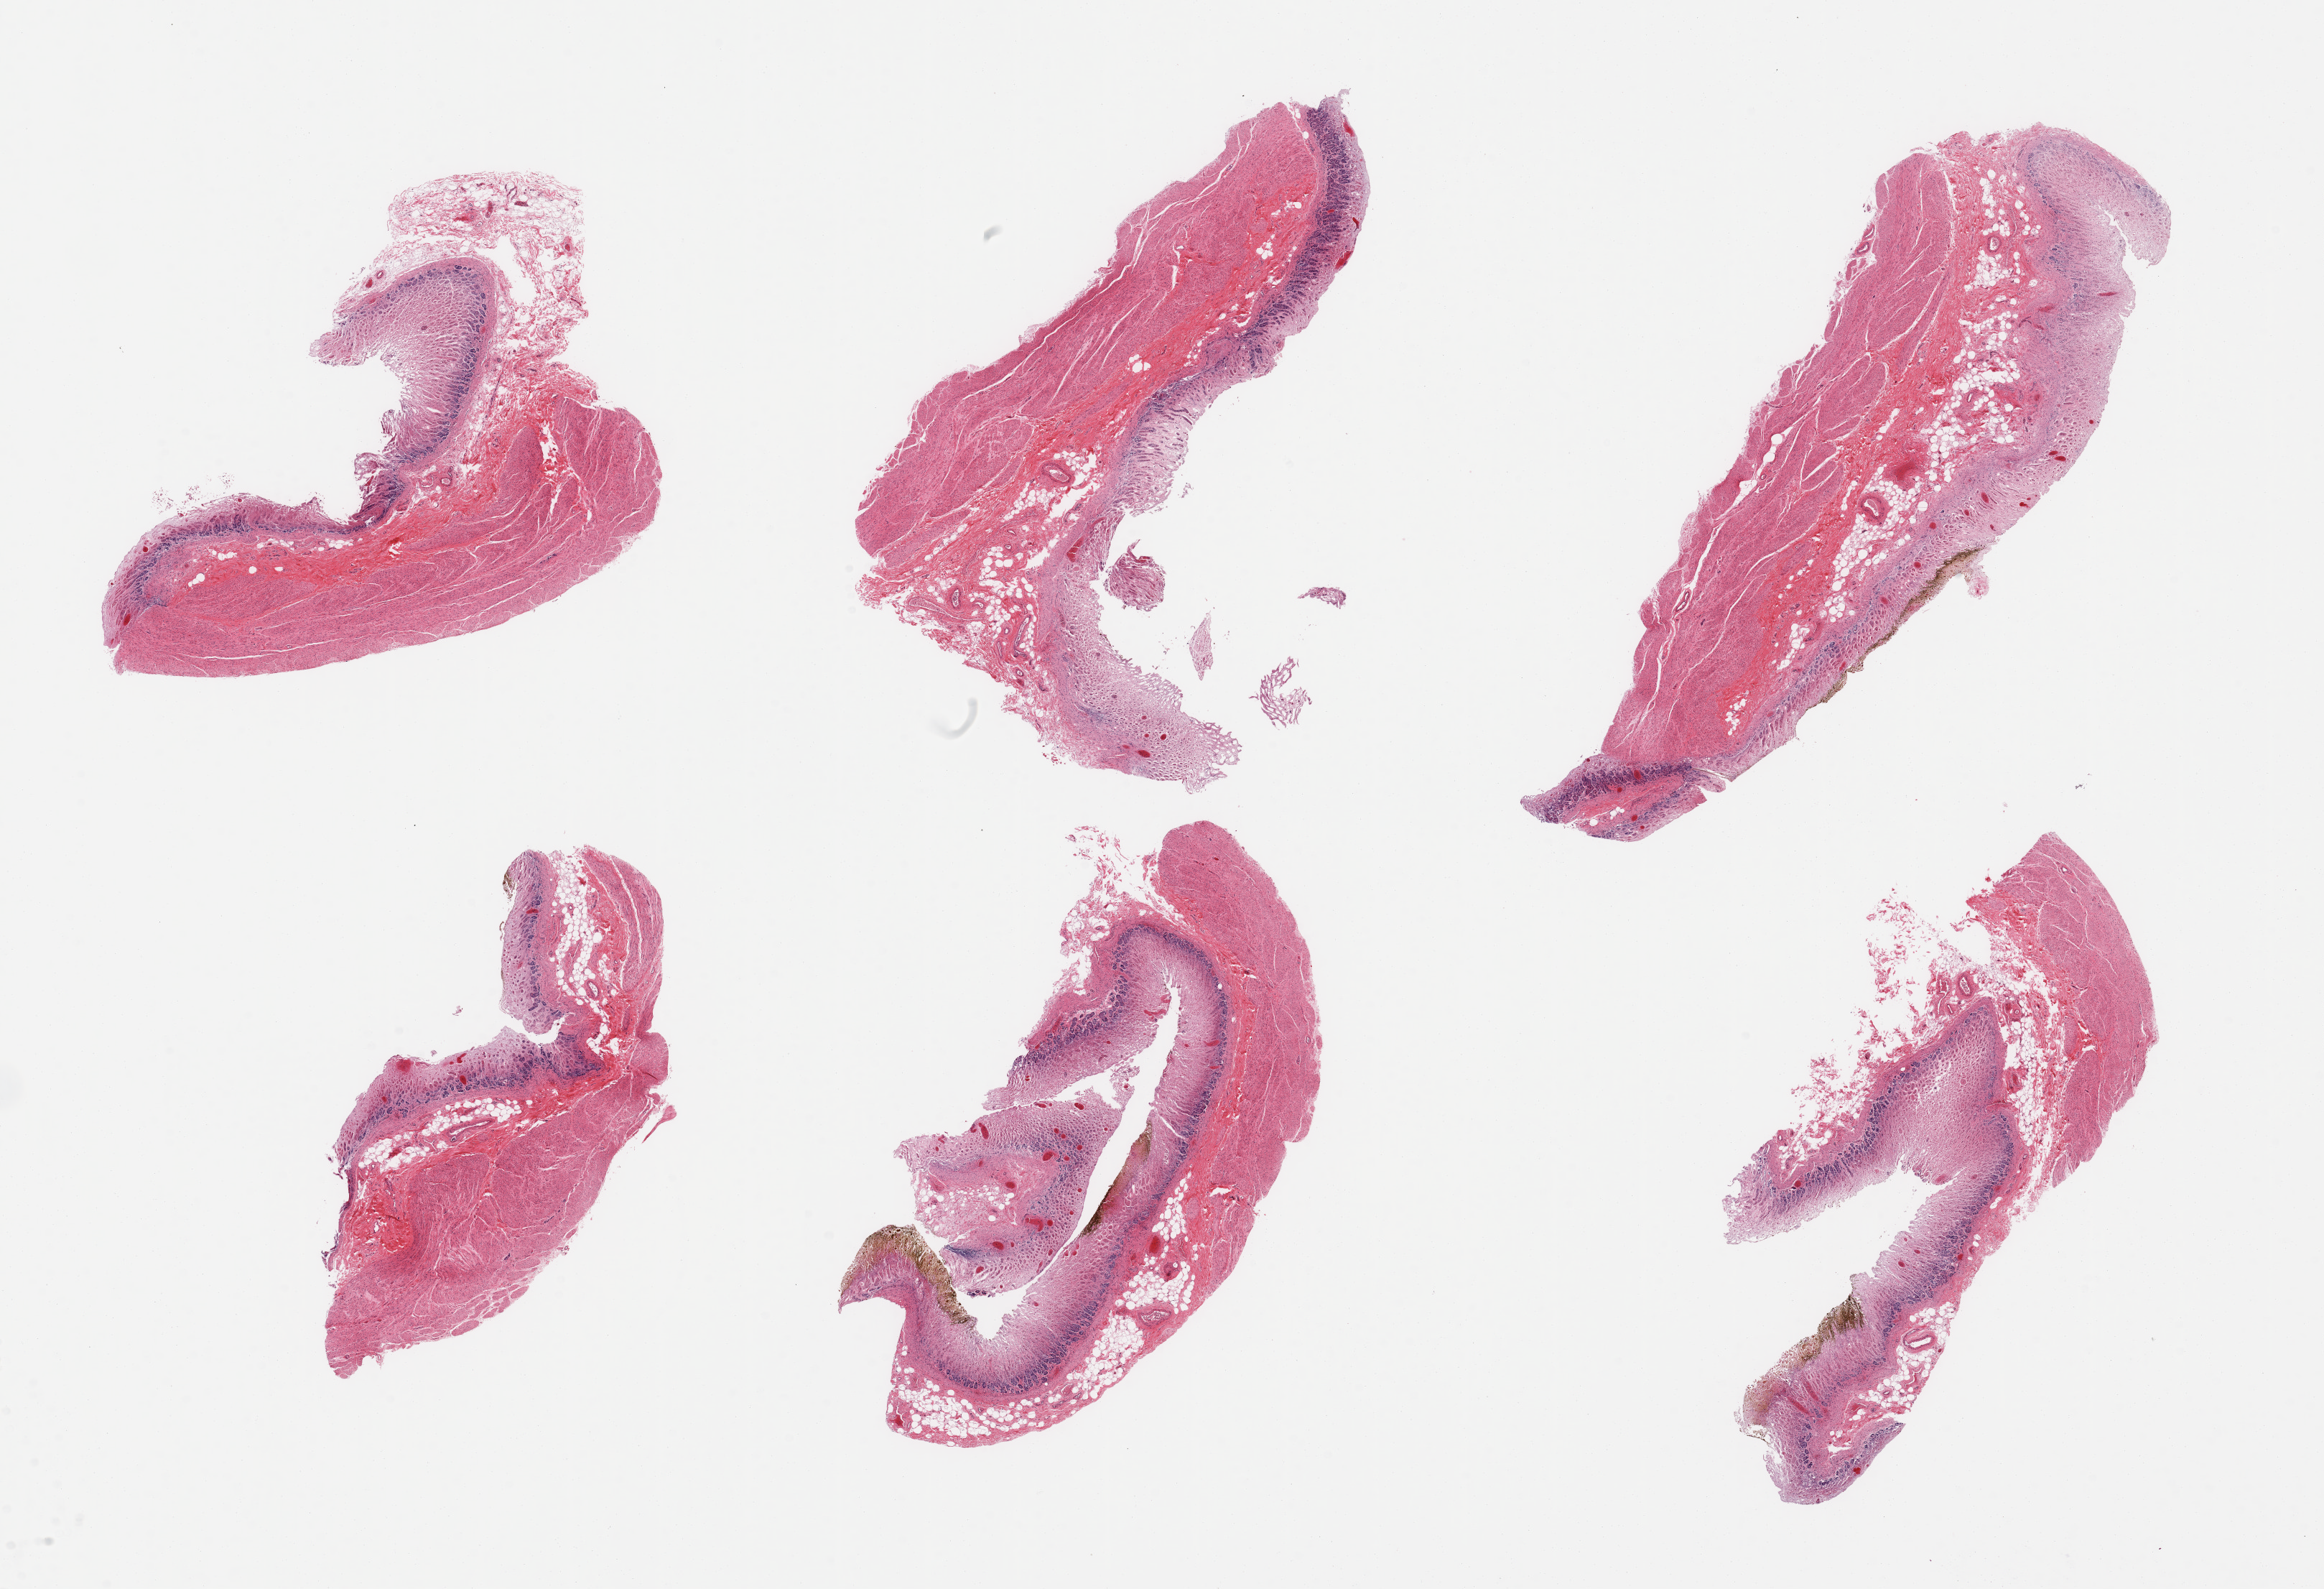
Hematoxylin and eosin (H&E) whole-slide image, brightfield — whole scanned area (about 25.6 x 17.5 mm) shown as a low-resolution overview. PAXgene-fixed, paraffin-embedded tissue. Sampled site (target tissue): stomach. Donor tissue sample.
Reviewer comment on this tissue sample: 6 pieces; mucosa largely autolyzed; muscu;aris preserved.